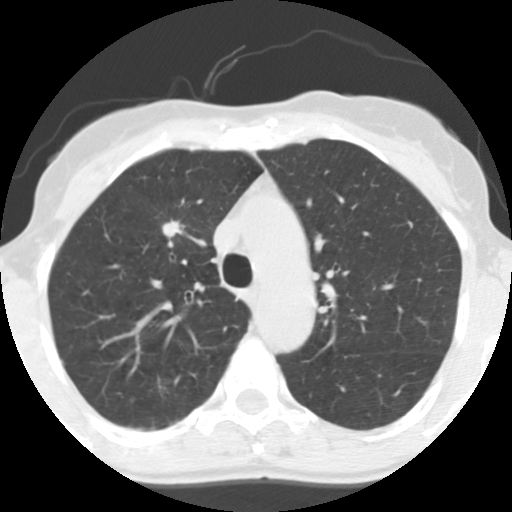
Low-dose screening chest CT, axial slice. Baseline screening round. Lung window (W 1500 / L -600 HU). Standard (soft-tissue) reconstruction kernel (STANDARD). Slice 43 of 130 in the series. 512 × 512 image matrix. Female, age 56 years at enrolment. Former smoker at enrolment.
• Expert-annotated lung lesion, bounding box (x1, y1, x2, y2) in pixels: (151, 211, 191, 250).
• Screening reader's record for this exam (one nodule recorded; not confirmed to be the boxed lesion): non-calcified nodule or mass ≥4 mm, right upper lobe, 12 × 9 mm, spiculated (stellate) margins, soft tissue attenuation.
• Official screen result: positive, change unspecified: nodule(s) >= 4 mm or enlarging nodule(s), mass(es), or other non-specific abnormalities suspicious for lung cancer.
• Participant outcome: lung cancer diagnosed 779 days after this screen — adenocarcinoma, NOS, right upper lobe, moderately differentiated (G2), stage IA (AJCC 6th edition), 19 mm at pathology.